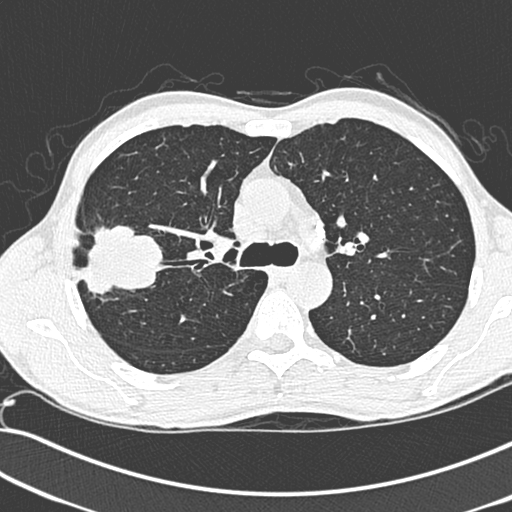
Low-dose screening chest CT, one axial slice. Position 200 of 281 along the scan axis. Lung window (W 1500 / L -600 HU). 1.3 mm slice thickness. 512 × 512 image matrix.
Outlined on this slice (outlined manually by an expert reader):
- lesion 1 (tumor, upper lobe of right lung): bounding box (x1, y1, x2, y2) in pixels: (76, 224, 163, 299)